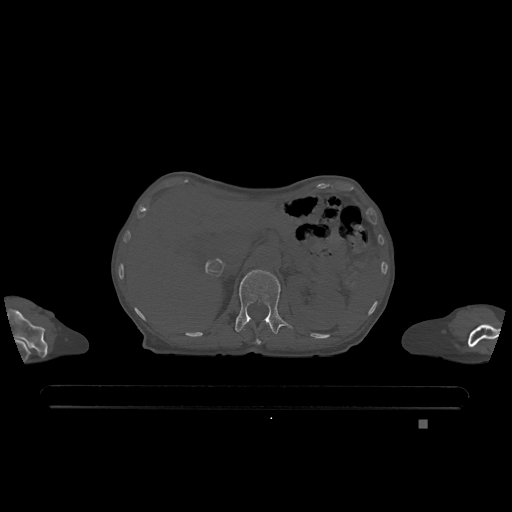
CT including the spine, one axial slice. Position 486 of 1317 along the scan axis. Bone window (W 1800 / L 400 HU). 0.5 mm slice thickness. 512 × 512 image matrix, field of view 500 × 500 mm. Female patient, age 74 years. From the clinical record (not read from this slice): primary cancer: lung.
Structures marked on this image (semi-automatic segmentation, software-assisted and operator-edited):
- L1 vertebra: bounding box [x1, y1, x2, y2] px = [235, 270, 293, 334]
- T12 vertebra: [243, 329, 261, 345]